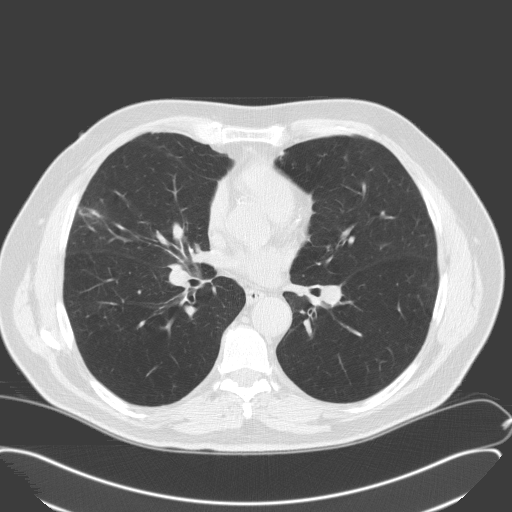
Chest CT (low-dose screening protocol), one axial image. Second screening round (one year after baseline). Lung window (W 1500 / L -600 HU). 120 kVp. Slice 85 of 175 in the series. 512 × 512 image matrix, field of view 400 × 400 mm. Male participant, aged 65 years at enrolment.
• Lesion marked by an expert reader, bounding box (x1, y1, x2, y2) in pixels: (61, 192, 116, 245).
• No non-calcified nodule or mass ≥4 mm was recorded by the screening reader at this exam.
• Official screen result: negative screen, minor abnormalities not suspicious for lung cancer.
• Lung cancer was diagnosed 346 days after this screen (after the third annual screen): adenocarcinoma, NOS, right middle lobe, moderately differentiated (G2), stage IA (AJCC 6th edition), 25 mm at pathology.